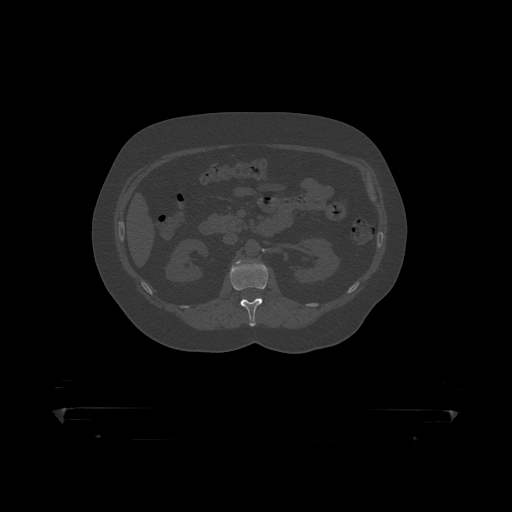
CT including the spine, one axial slice; slice 138 of 390 in the series (ordered by position); 120 kVp; bone window (W 1800 / L 400 HU); 512 × 512 image matrix, field of view 650 × 650 mm. Patient: male, 60 years. From the clinical record (not read from this slice): primary cancer: prostate.
Structures marked on this image (semi-automatically segmented with operator editing):
- L1 vertebra: bounding box (x1, y1, x2, y2) in pixels: (231, 260, 269, 319)